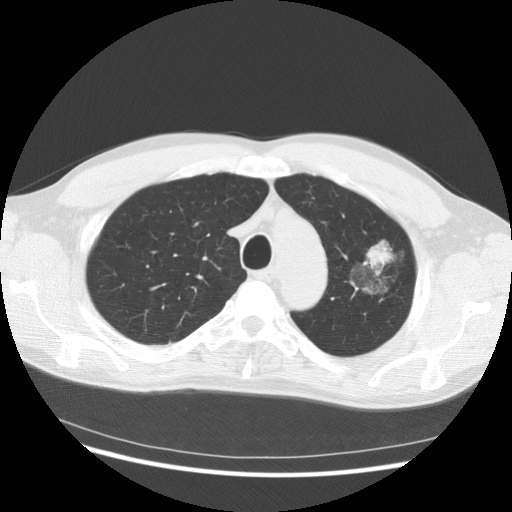
Low-dose screening chest CT, one axial slice; slice 110 of 145 in the series (ordered by position); reconstruction kernel STANDARD; 140 kVp; lung window (W 1500 / L -600 HU); 2.5 mm slice thickness; 512 × 512 image matrix, field of view 370 × 370 mm.
Structures marked on this image (expert manual segmentation):
- lesion 1 (tumor, upper lobe of left lung): box from (x=367, y=242) to (x=391, y=265) px